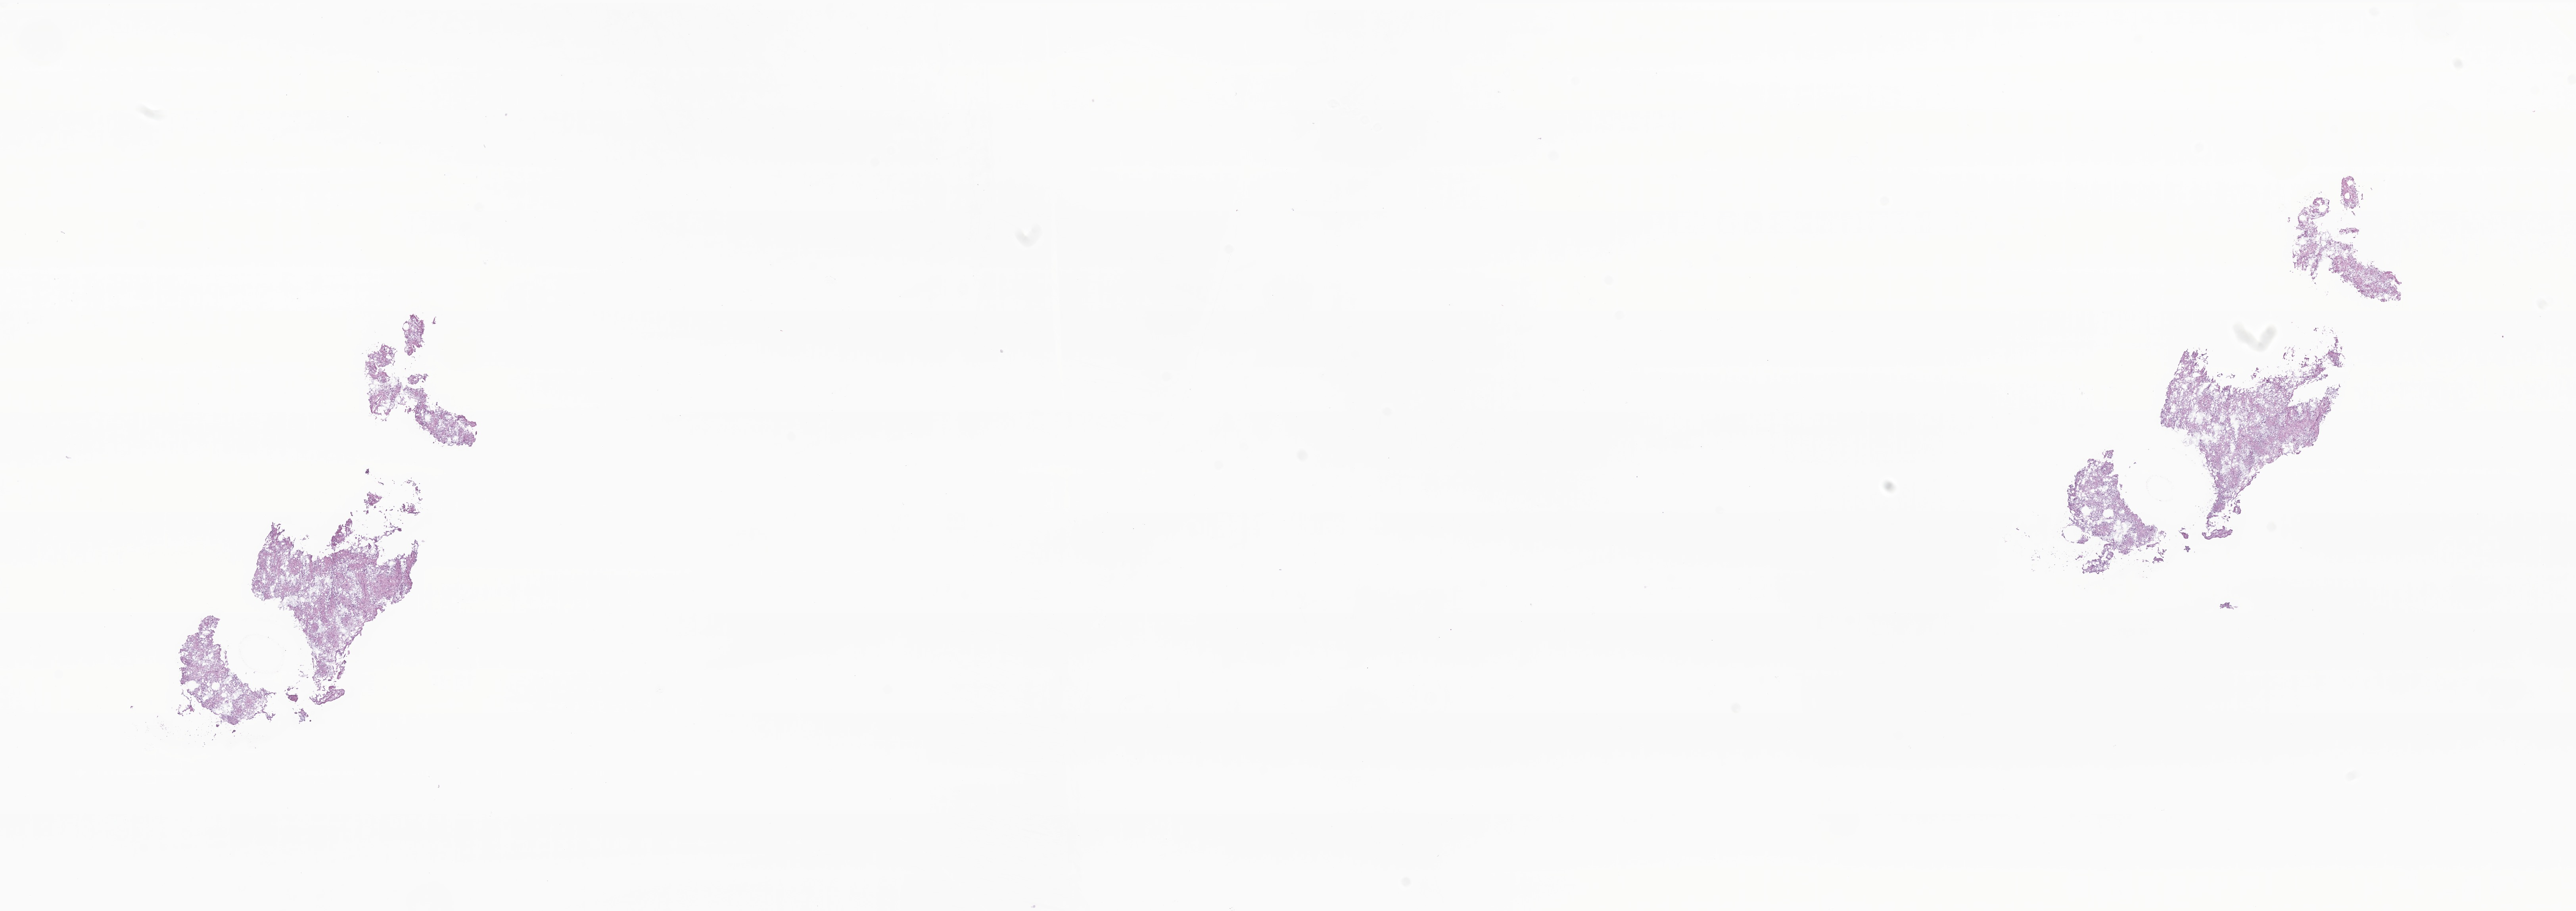
Digitized haematoxylin and eosin-stained section of tumor tissue from the cerebellum, low-resolution overview of the scanned area, about 27.4 x 9.7 mm, frozen section. Patient male; age 57 months (4 years 9 months).
Diagnosis (ICD-O-3 morphology term): Pilocytic astrocytoma.